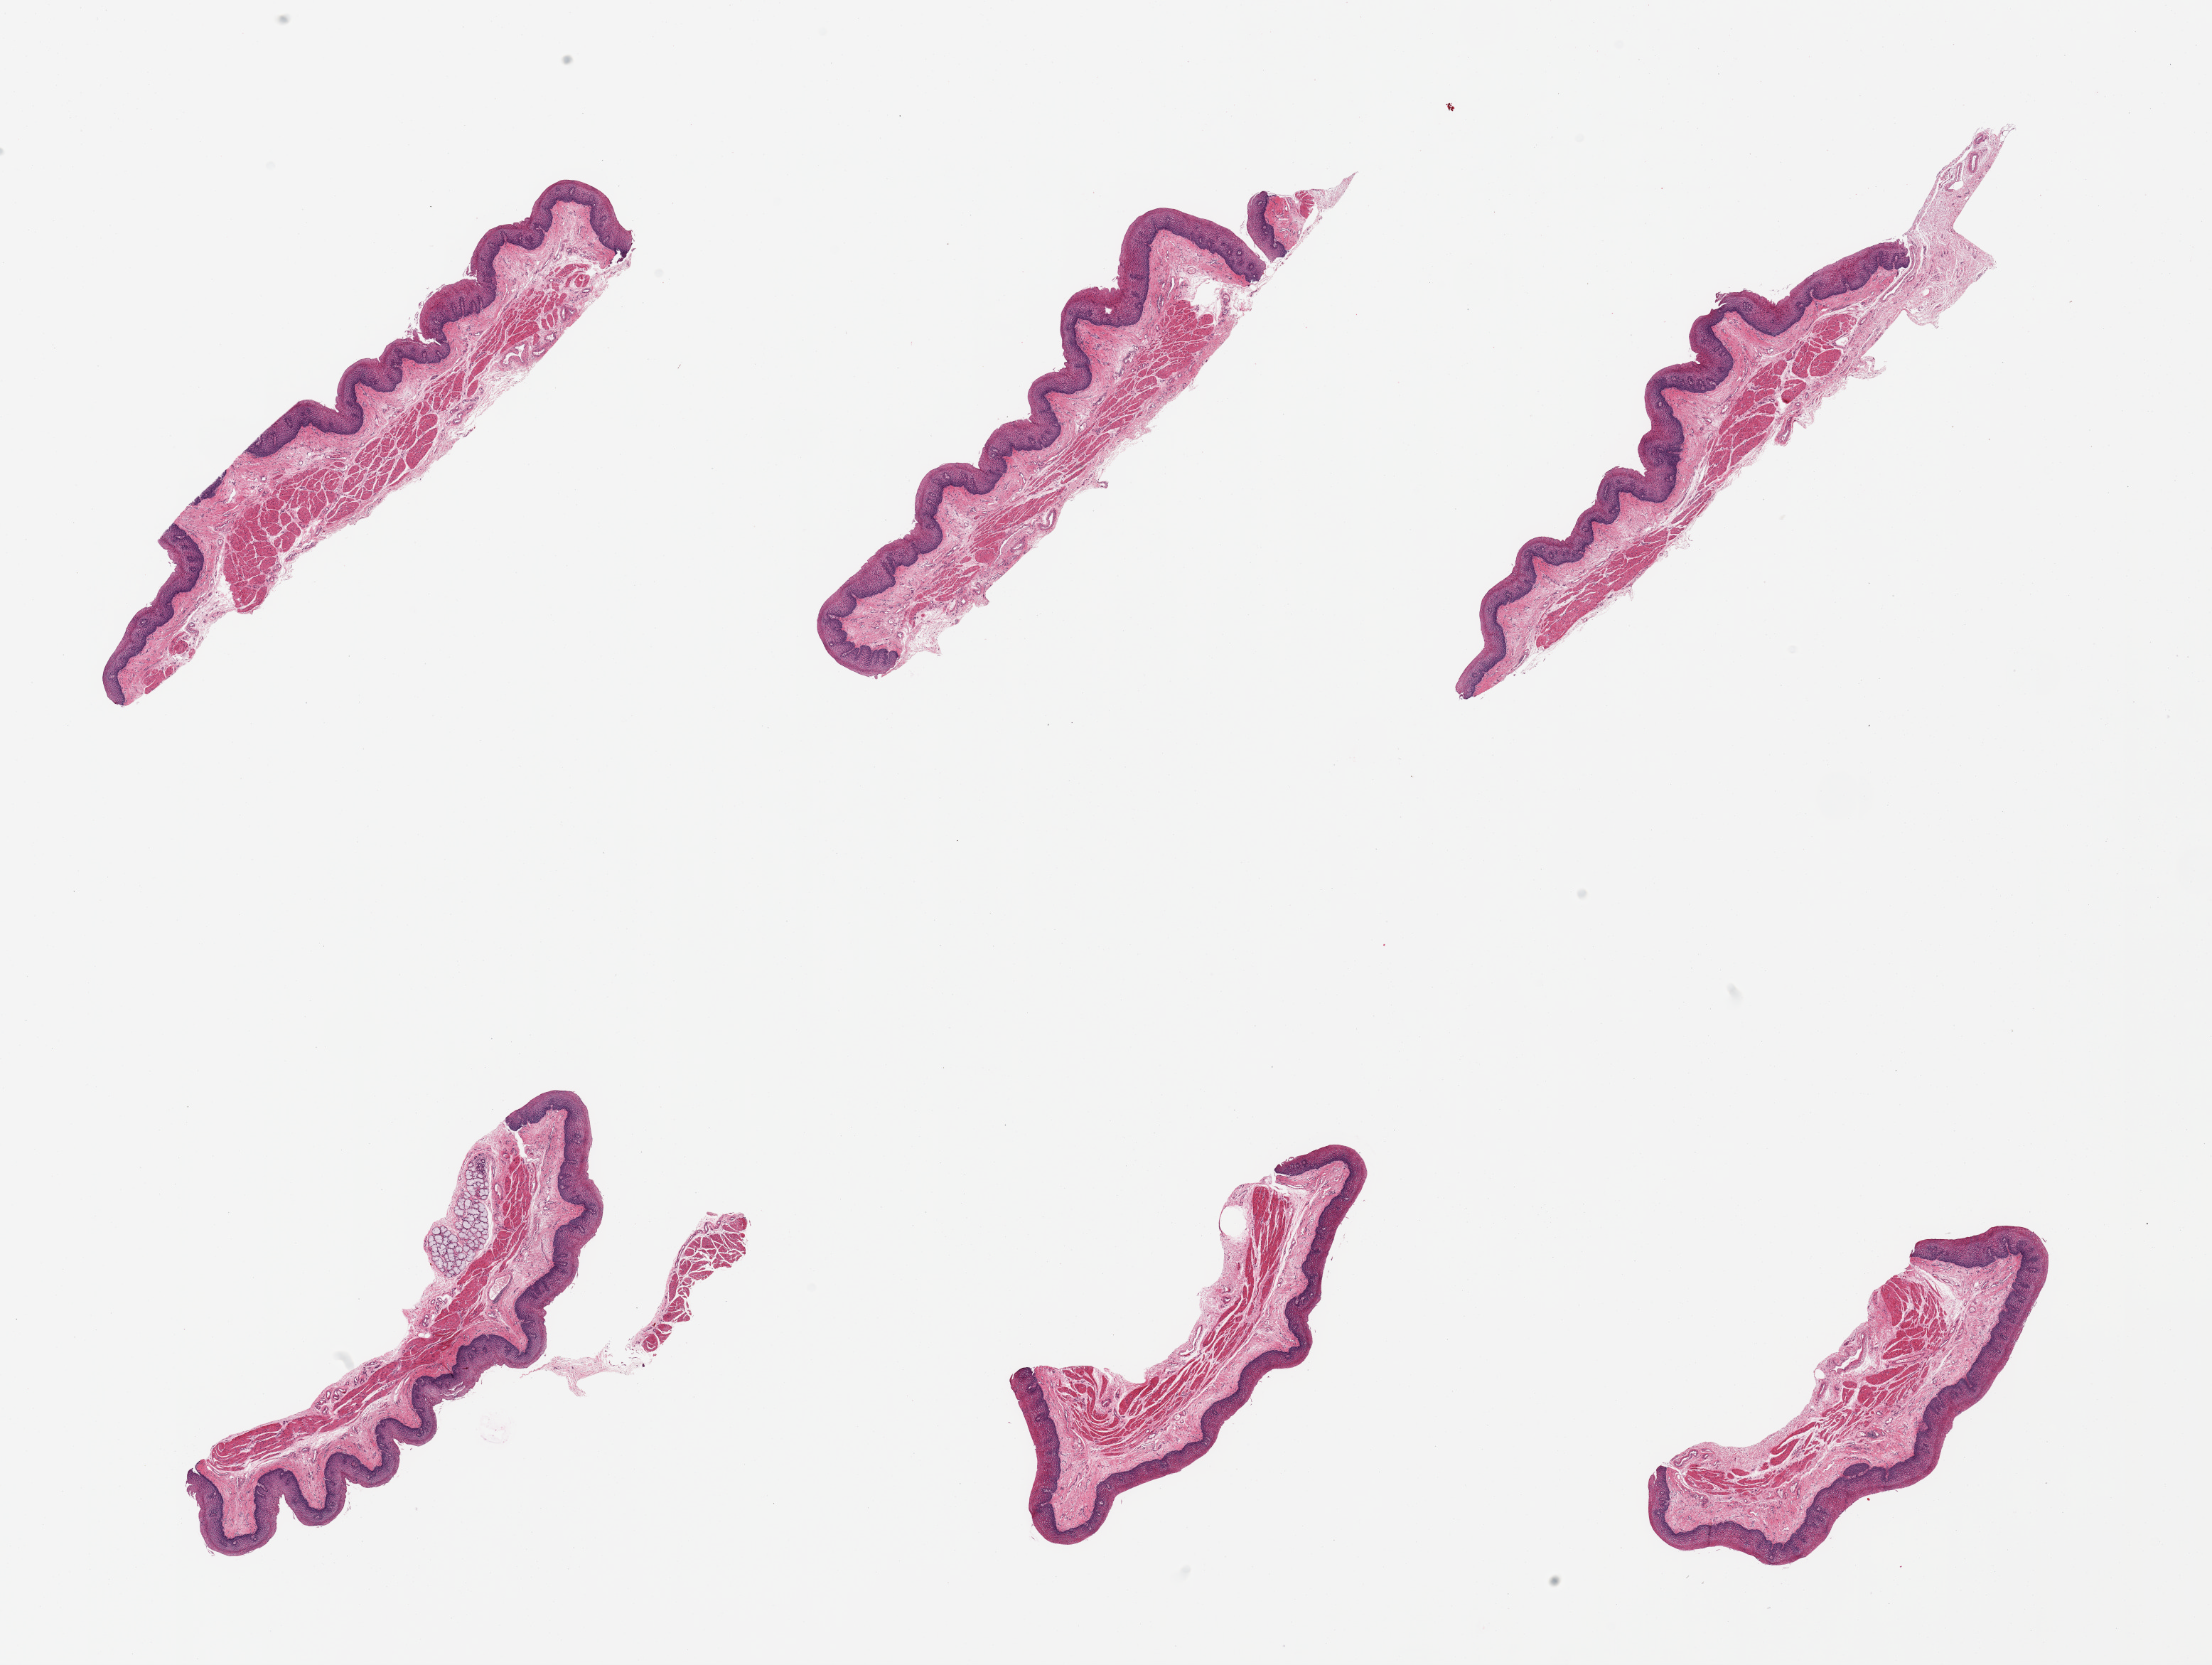
Digitized H&E-stained section, shown as a low-resolution overview of the whole scanned area (about 24.6 x 18.5 mm), PAXgene-fixed, paraffin-embedded tissue, target tissue: esophageal mucous membrane, tissue donor sample. Donor: female.
* review note (as recorded): 6 pieces, squamous mucosa is ~0.5mm, ~30% thickness